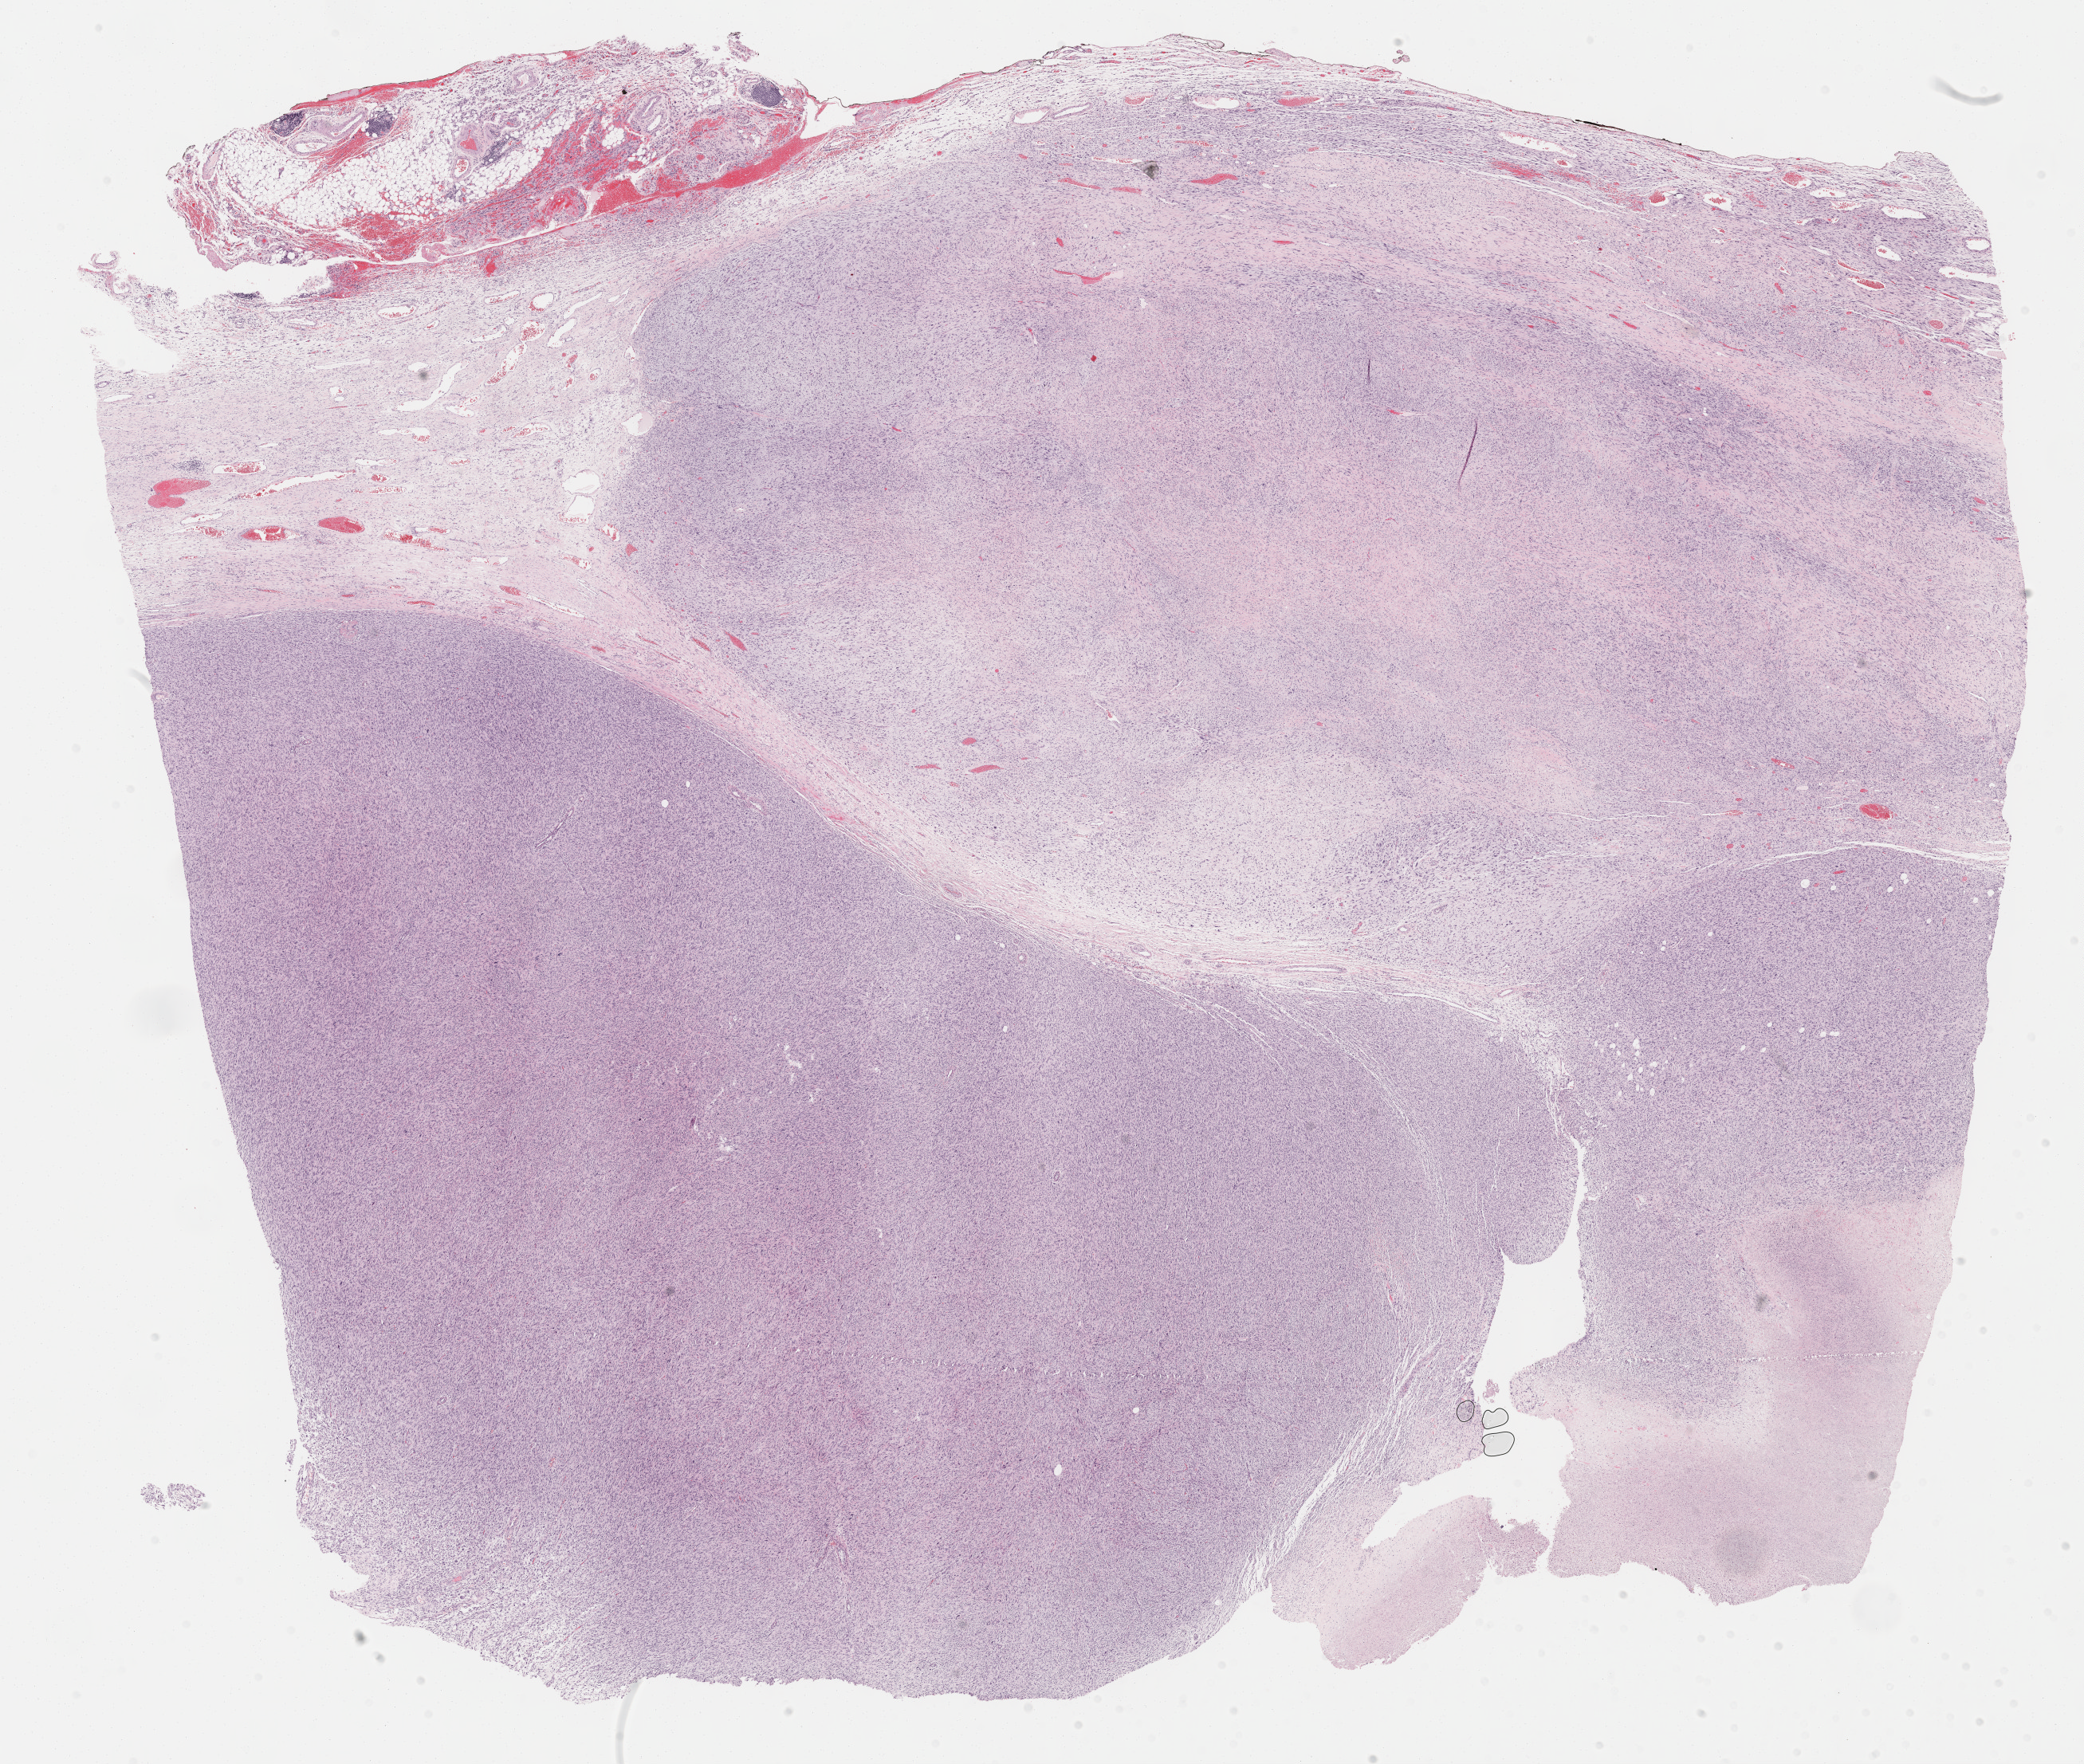
Digitized H&E-stained tissue section (whole slide), whole scanned area (about 21.1 x 17.9 mm) shown as a low-resolution overview; formalin-fixed paraffin-embedded (FFPE) diagnostic section; connective, subcutaneous and other soft tissues, primary tumour sample. Patient: female, age at initial diagnosis 63 years.
Pathologic diagnosis: Malignant fibrous histiocytoma (connective, subcutaneous and other soft tissues of thorax).